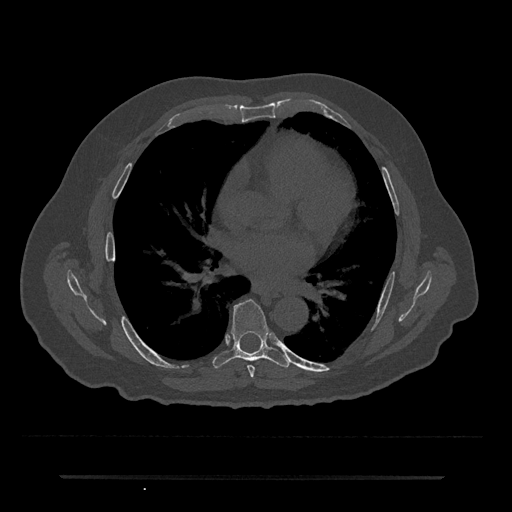
CT including the spine, one axial slice. Position 396 of 797 along the scan axis. Reconstruction kernel Br40s/3. Bone window (W 1800 / L 400 HU). 0.5 mm slice thickness. 512 × 512 image matrix, field of view 437 × 437 mm. Patient: male, 69 years. Case-level facts recorded for this patient, not image findings: primary cancer: prostate.
Annotated regions visible in this slice (semi-automatically segmented with operator editing):
- T6 vertebra: bounding box <248,365,255,377> (left, top, right, bottom; pixels)
- T7 vertebra: <213,299,290,368>